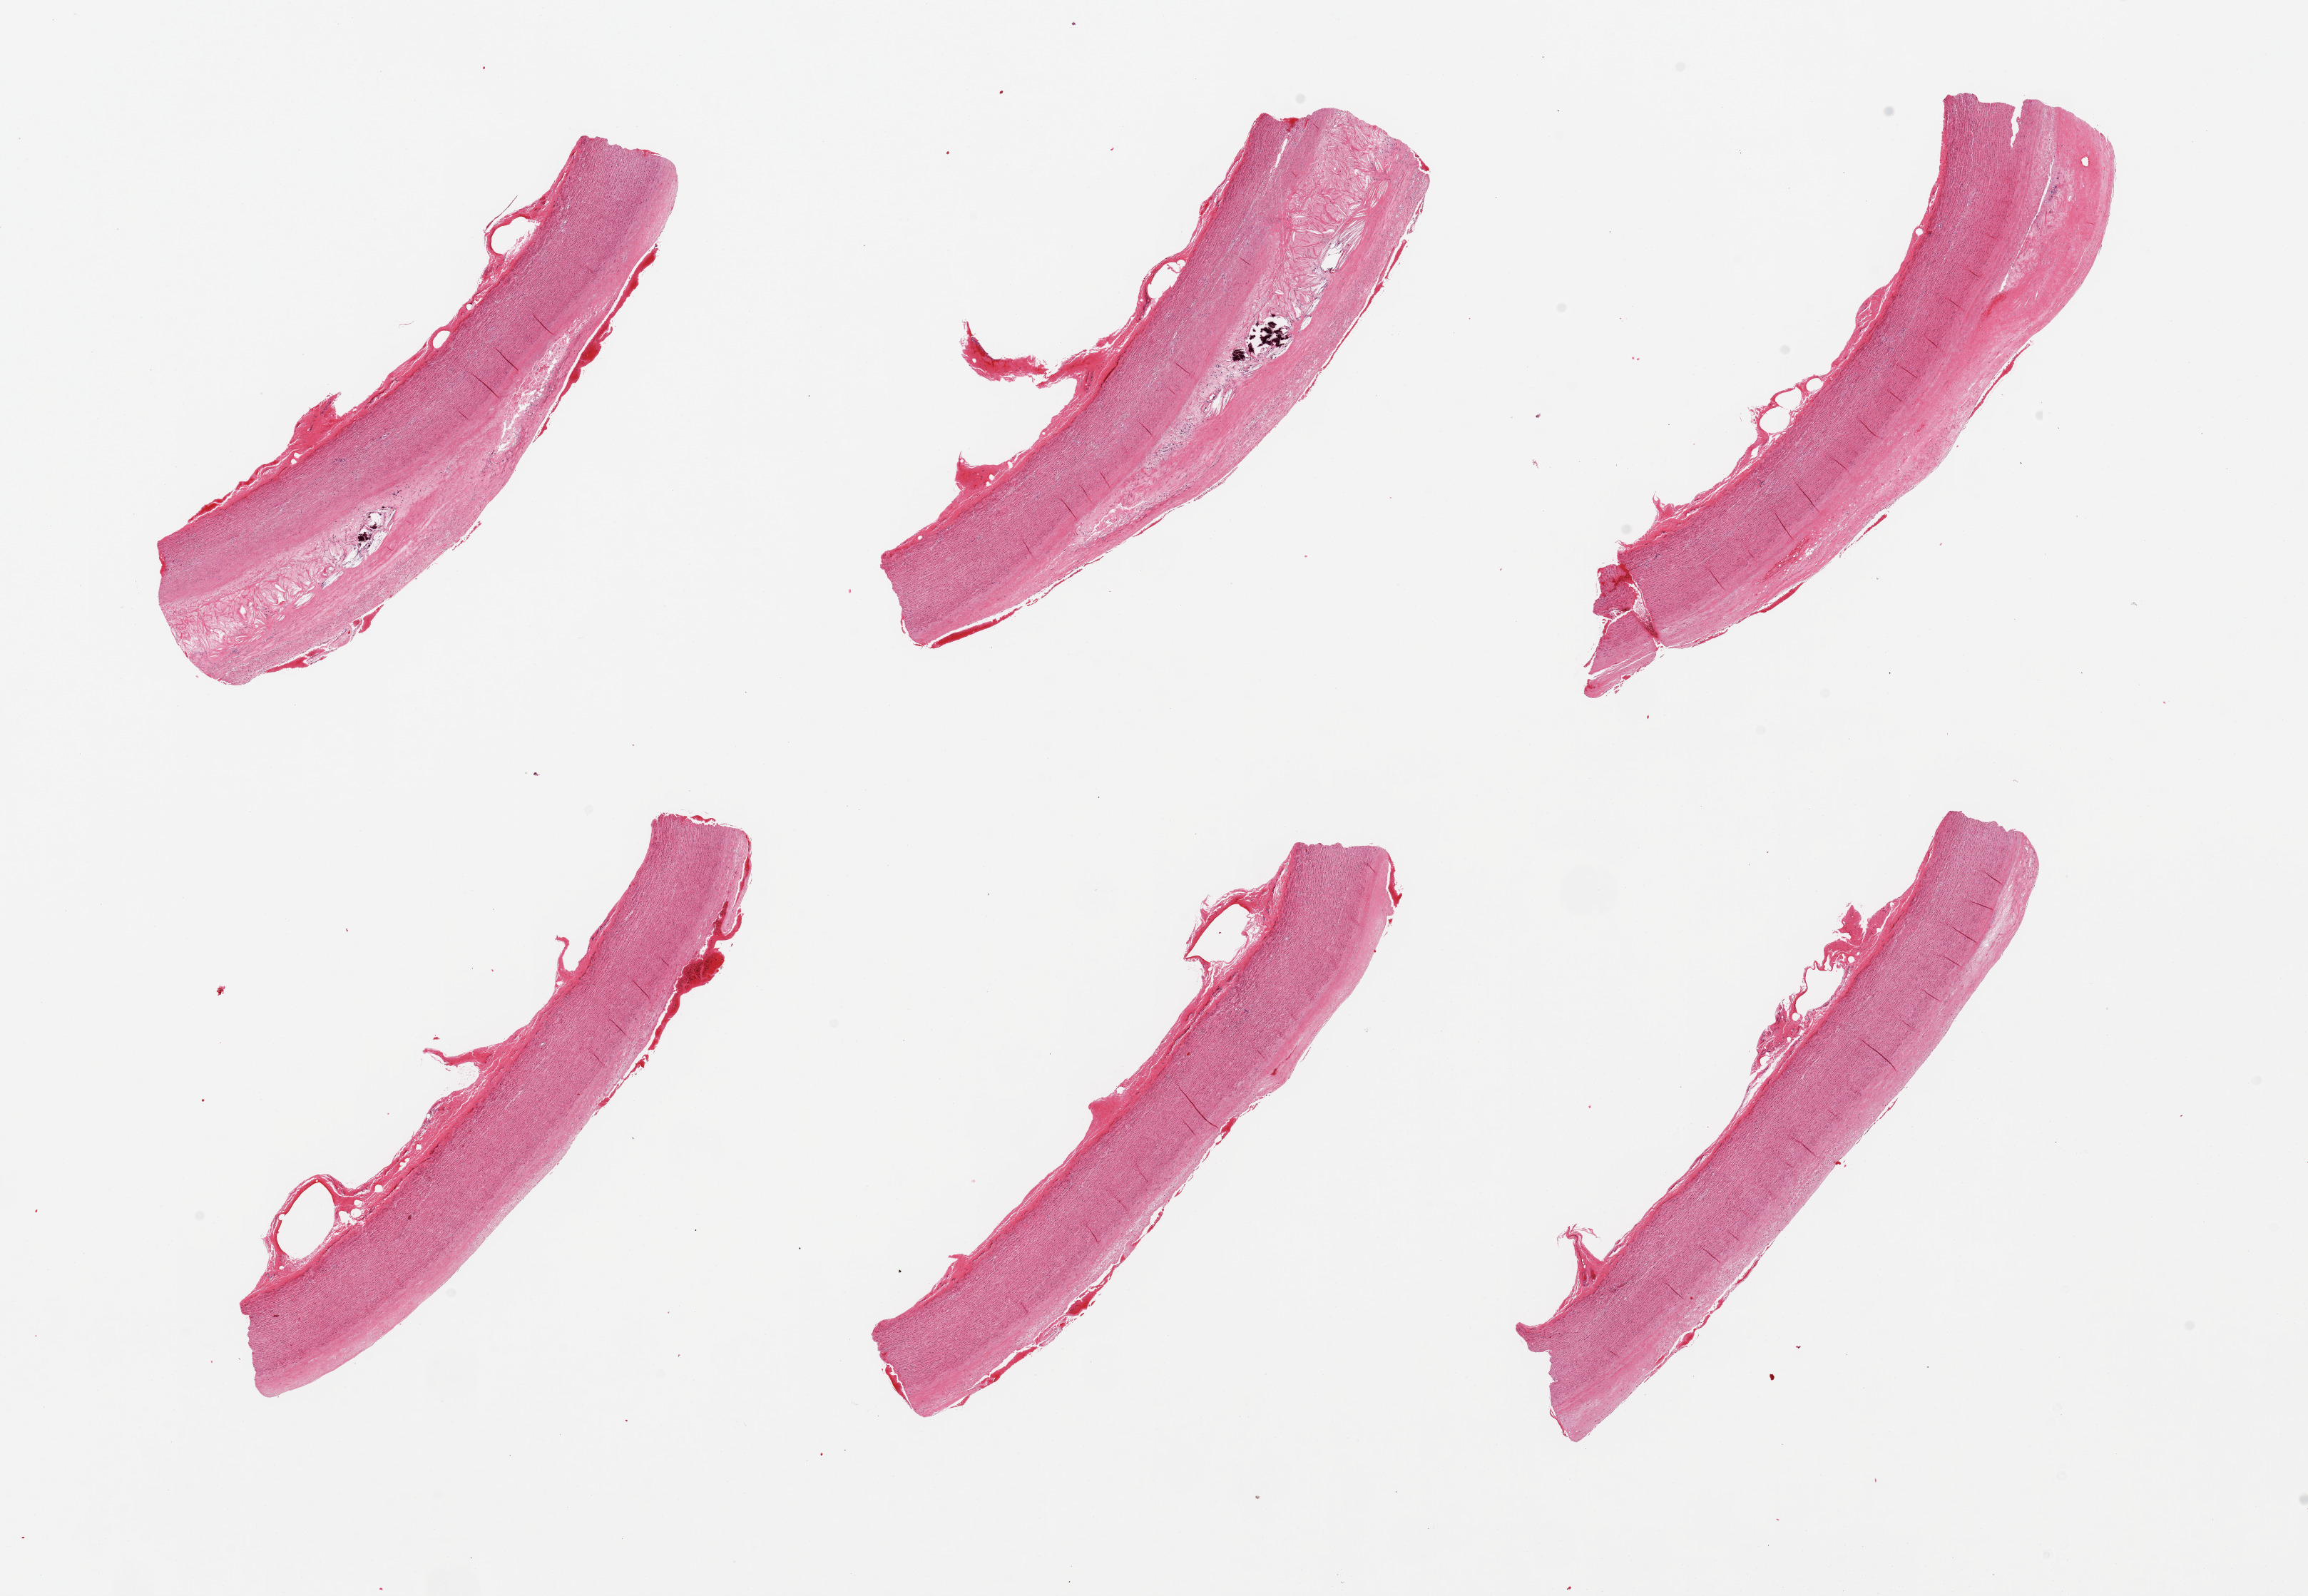
Digitized H&E-stained section, a low-resolution overview of the entire scanned area, about 25.6 x 17.7 mm (acquisition: 20x scan); PAXgene-fixed paraffin-embedded (PFPE) section; sampled site (target tissue): aorta; donor tissue sample.
Pathologist's review note for this sample: 6 pieces; calcific atherosclerosis.